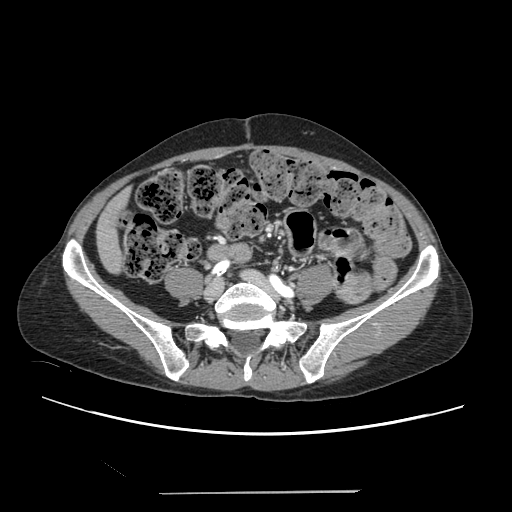
Contrast-enhanced abdominal CT, one axial slice. Position 16 of 240 along the scan axis. 120 kVp. Soft-tissue window (W 400 / L 40 HU). 1.25 mm slice thickness. 512 × 512 image matrix, field of view 371 × 371 mm. Female patient, age 60 years. From the clinical record (not read from this slice): diagnosis: colorectal cancer liver metastases, imaged before liver resection; multiple liver metastases: no; largest metastasis: 1.5 cm; disease in both lobes: no.
Outlined on this slice (manually delineated by an expert):
- liver: bounding box <98,196,126,271> (left, top, right, bottom; pixels)
- planned liver remnant (the part of the liver to remain after resection): <98,196,126,271>